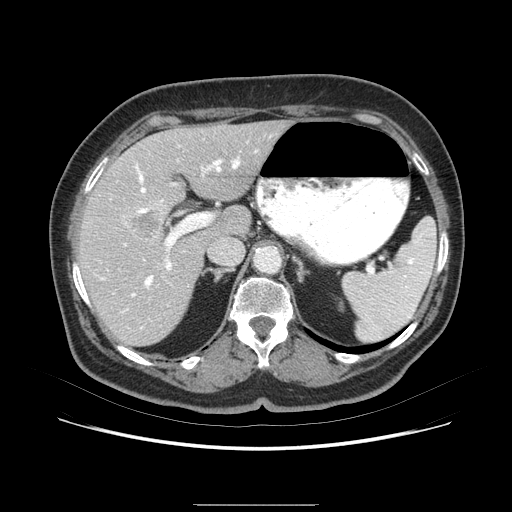
Contrast-enhanced abdominal CT (liver protocol), one axial slice. Slice 48 of 79 in the series (ordered by position). 120 kVp. Soft-tissue window (W 400 / L 40 HU). 2.5 mm slice thickness. 512 × 512 image matrix. From the clinical record (not read from this slice): diagnosis: hepatocellular carcinoma (patient treated with transarterial chemoembolisation; whether this scan precedes or follows treatment is not stated here); TNM stage (as recorded): Stage-I; Child-Pugh class: A; tumour differentiation: poorly differentiated; tumour nodularity: uninodular.
Outlined on this slice (semi-automatically segmented with operator editing):
- liver parenchyma outside the tumour (the mass and vessels are separate outlines, so this box may not span the whole liver): bounding box (x1, y1, x2, y2) in pixels: (74, 124, 296, 348)
- mass: (133, 208, 170, 233)
- liver vessels: (118, 151, 258, 324)